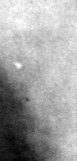
Crop from a digitized film mammogram around one marked abnormality, left breast, CC view.
- Calcifications, morphology punctate; BI-RADS assessment category 2; subtlety rating 4 on a 1 (subtle) to 5 (obvious) scale; benign without callback (not worked up further).